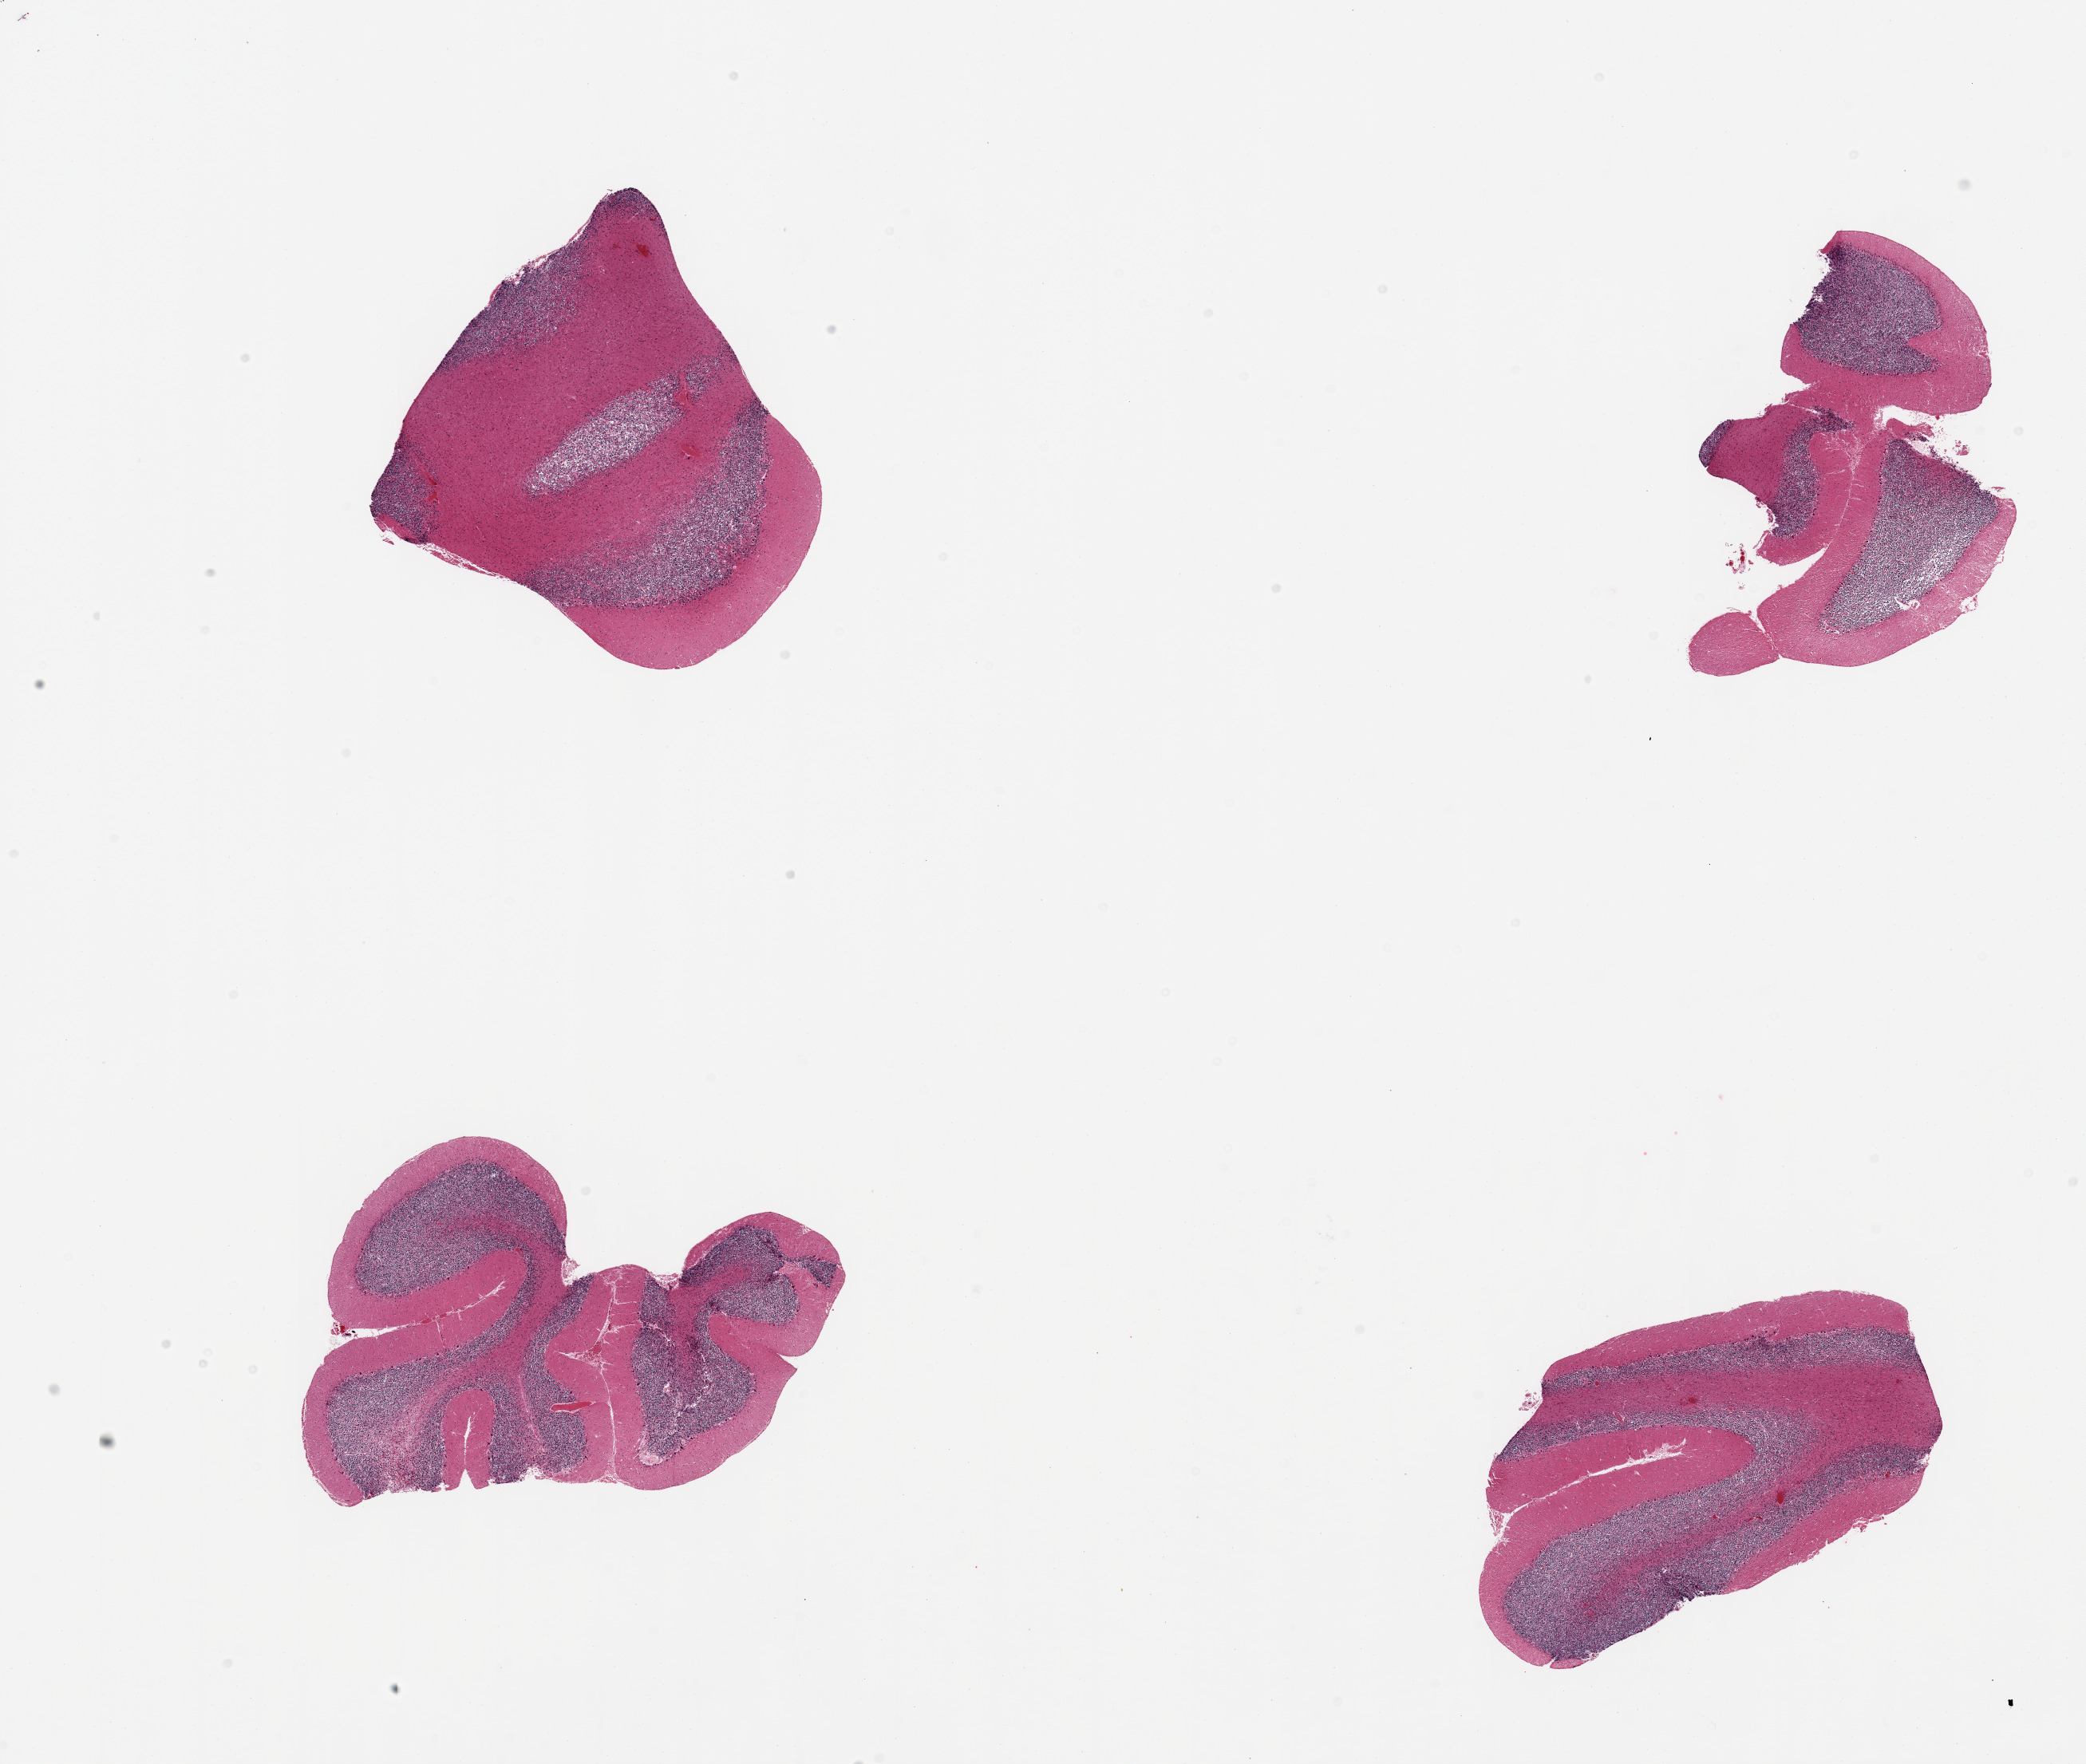
Whole-slide image, H&E stain, brightfield, low-resolution overview of the scanned area, about 20.7 x 17.5 mm (from a 20x scan), PAXgene-fixed paraffin-embedded (PFPE) section, section of cerebellum (target tissue), tissue donor sample. Donor: male.
- pathologist's review note for this sample: 4 pieces, no abnormalities